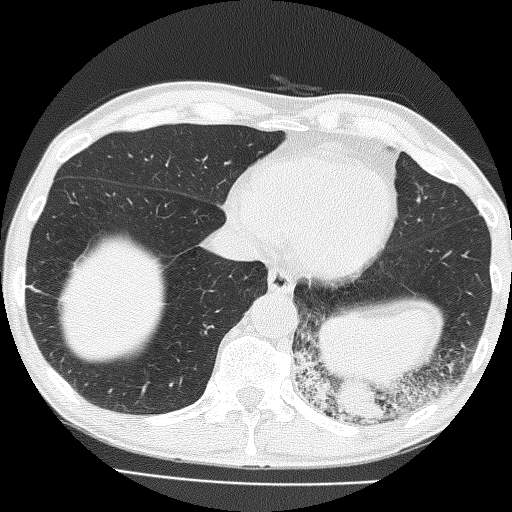
Low-dose screening chest CT, one axial slice; slice 48 of 160 in the series (ordered by position); reconstruction kernel FC51; lung window (W 1500 / L -600 HU); 2 mm slice thickness; 512 × 512 image matrix, field of view 324 × 324 mm.
Structures marked on this image (expert manual segmentation):
- lesion 1 (tumor, lower lobe of left lung): bounding box (x1, y1, x2, y2) in pixels: (333, 378, 384, 420)